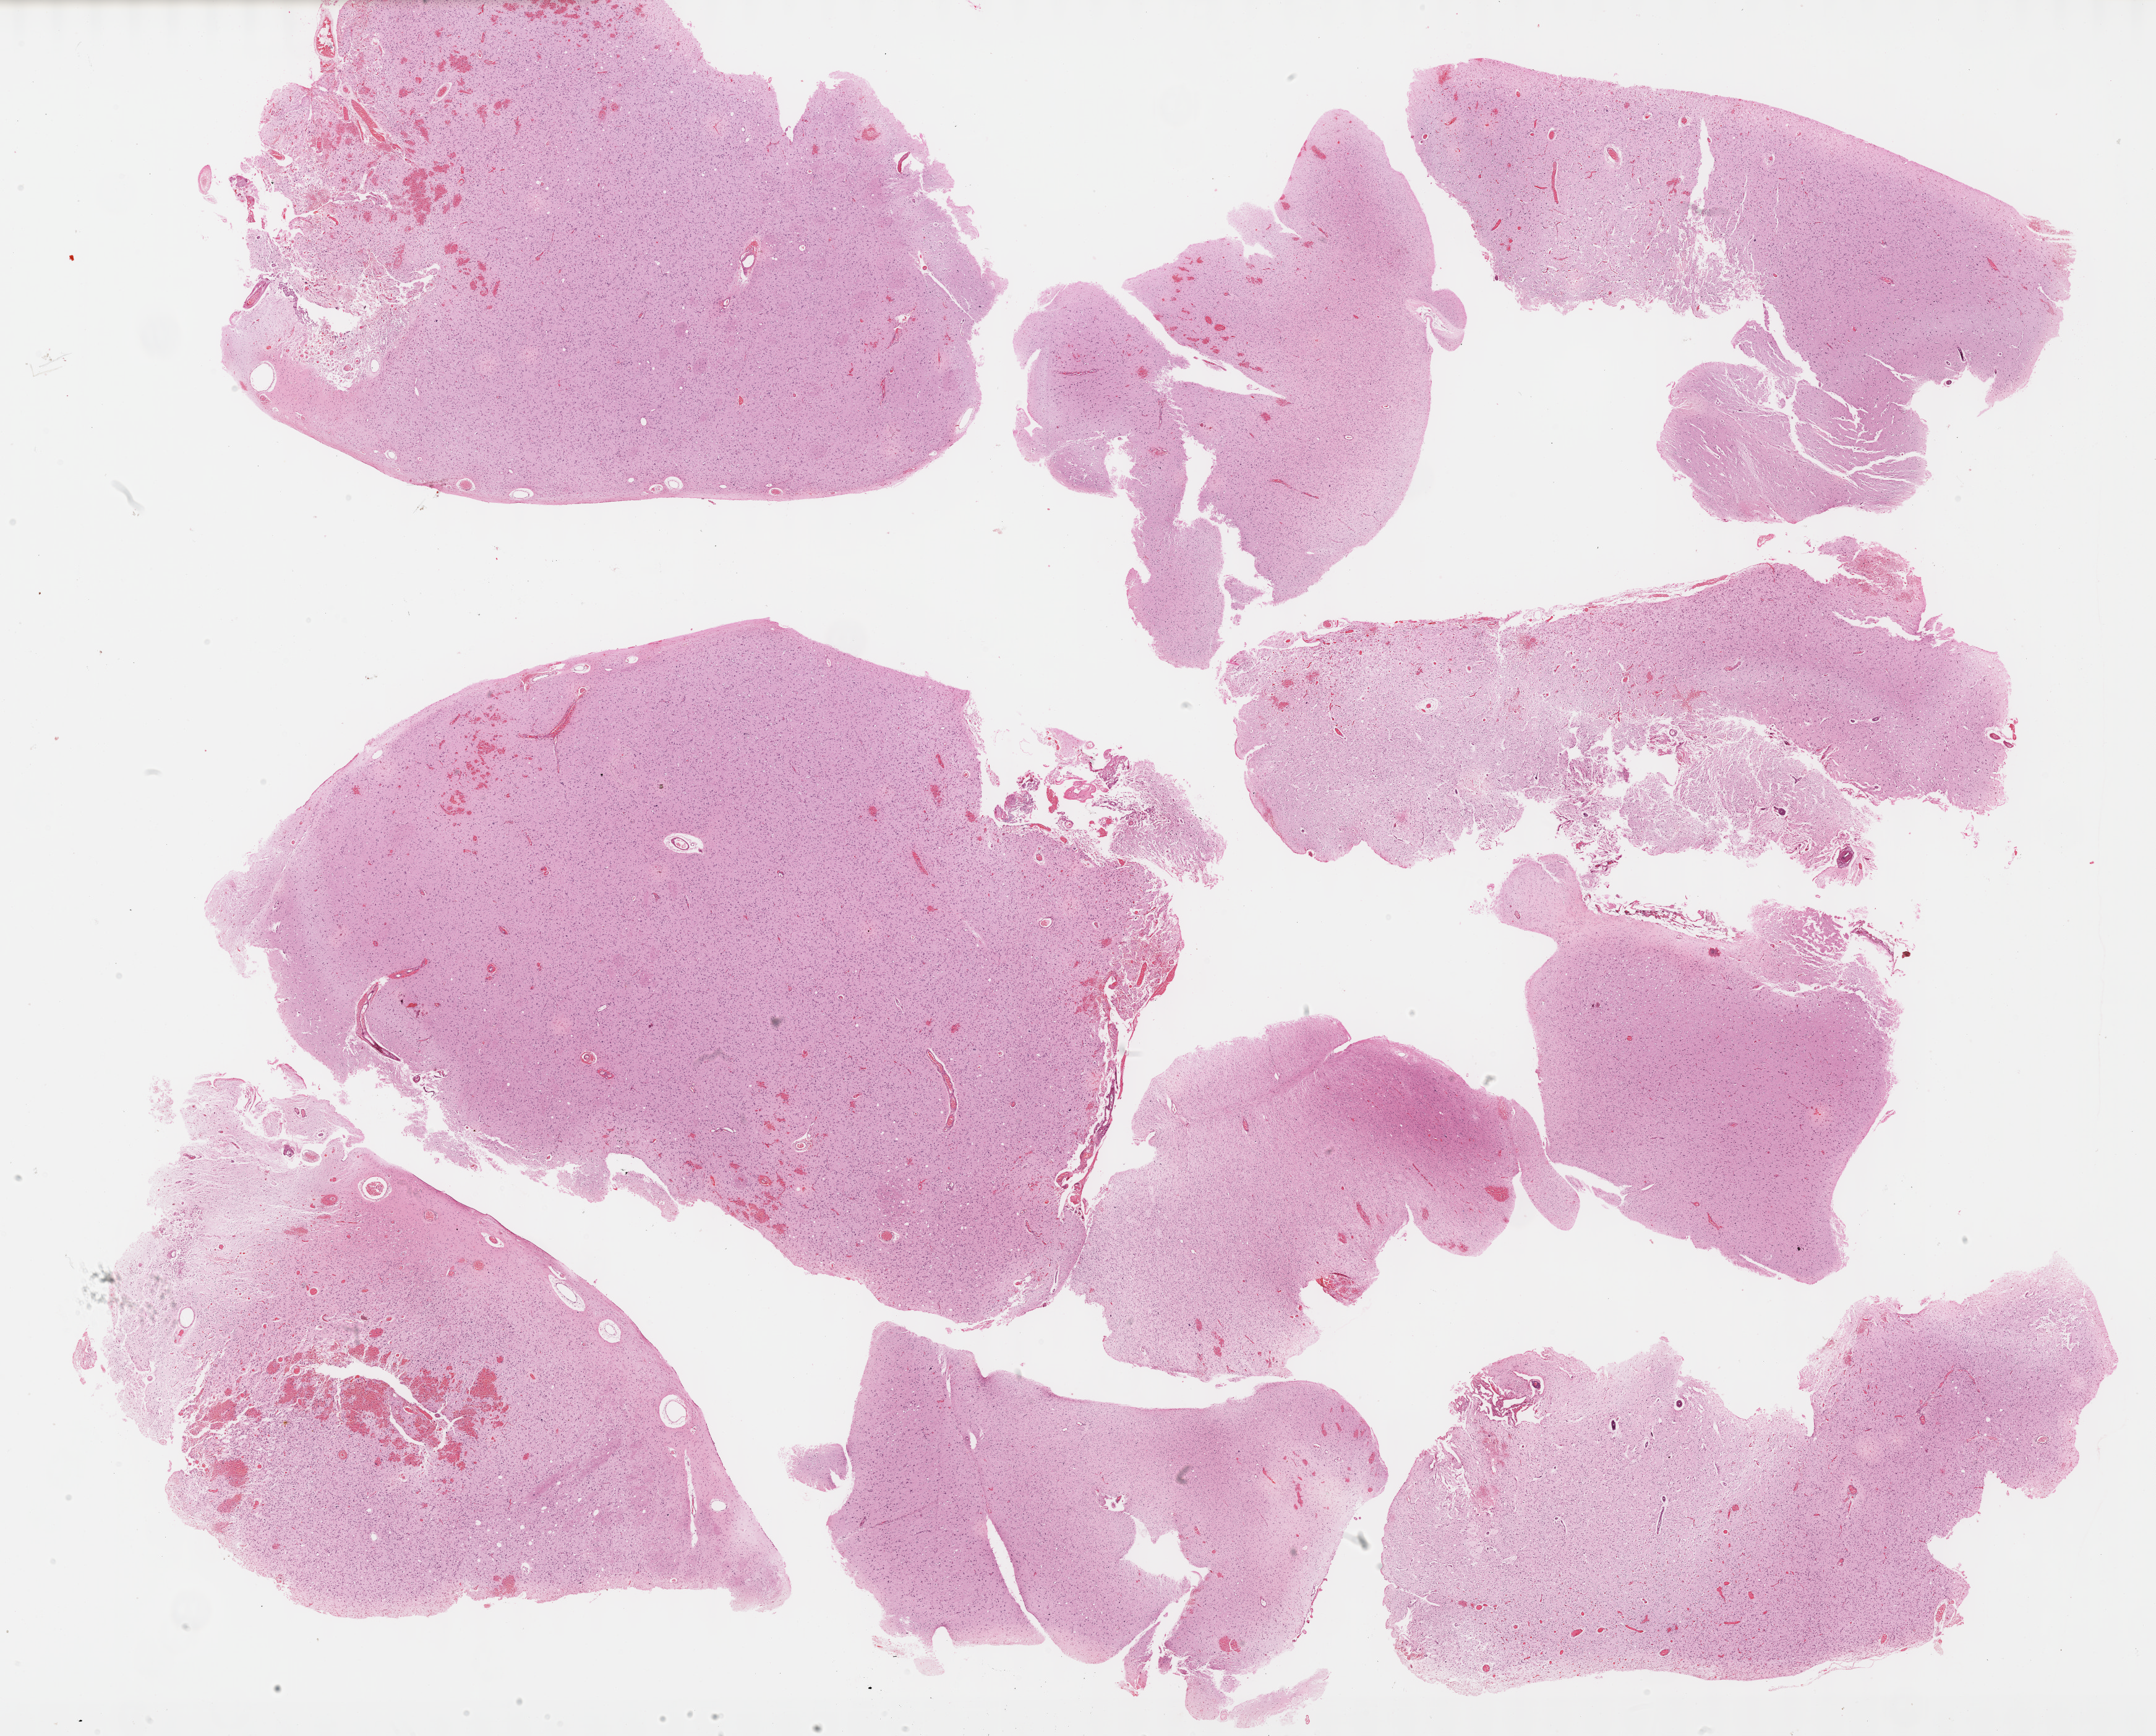
Digitized H&E tissue section (whole slide) — low-resolution overview of the scanned area, about 28.2 x 22.7 mm. Formalin-fixed paraffin-embedded (FFPE) diagnostic section. Sample: recurrent tumour, brain. Male, age 27 years at initial diagnosis.
- this section: recurrent tumour
- patient diagnosis: Mixed glioma